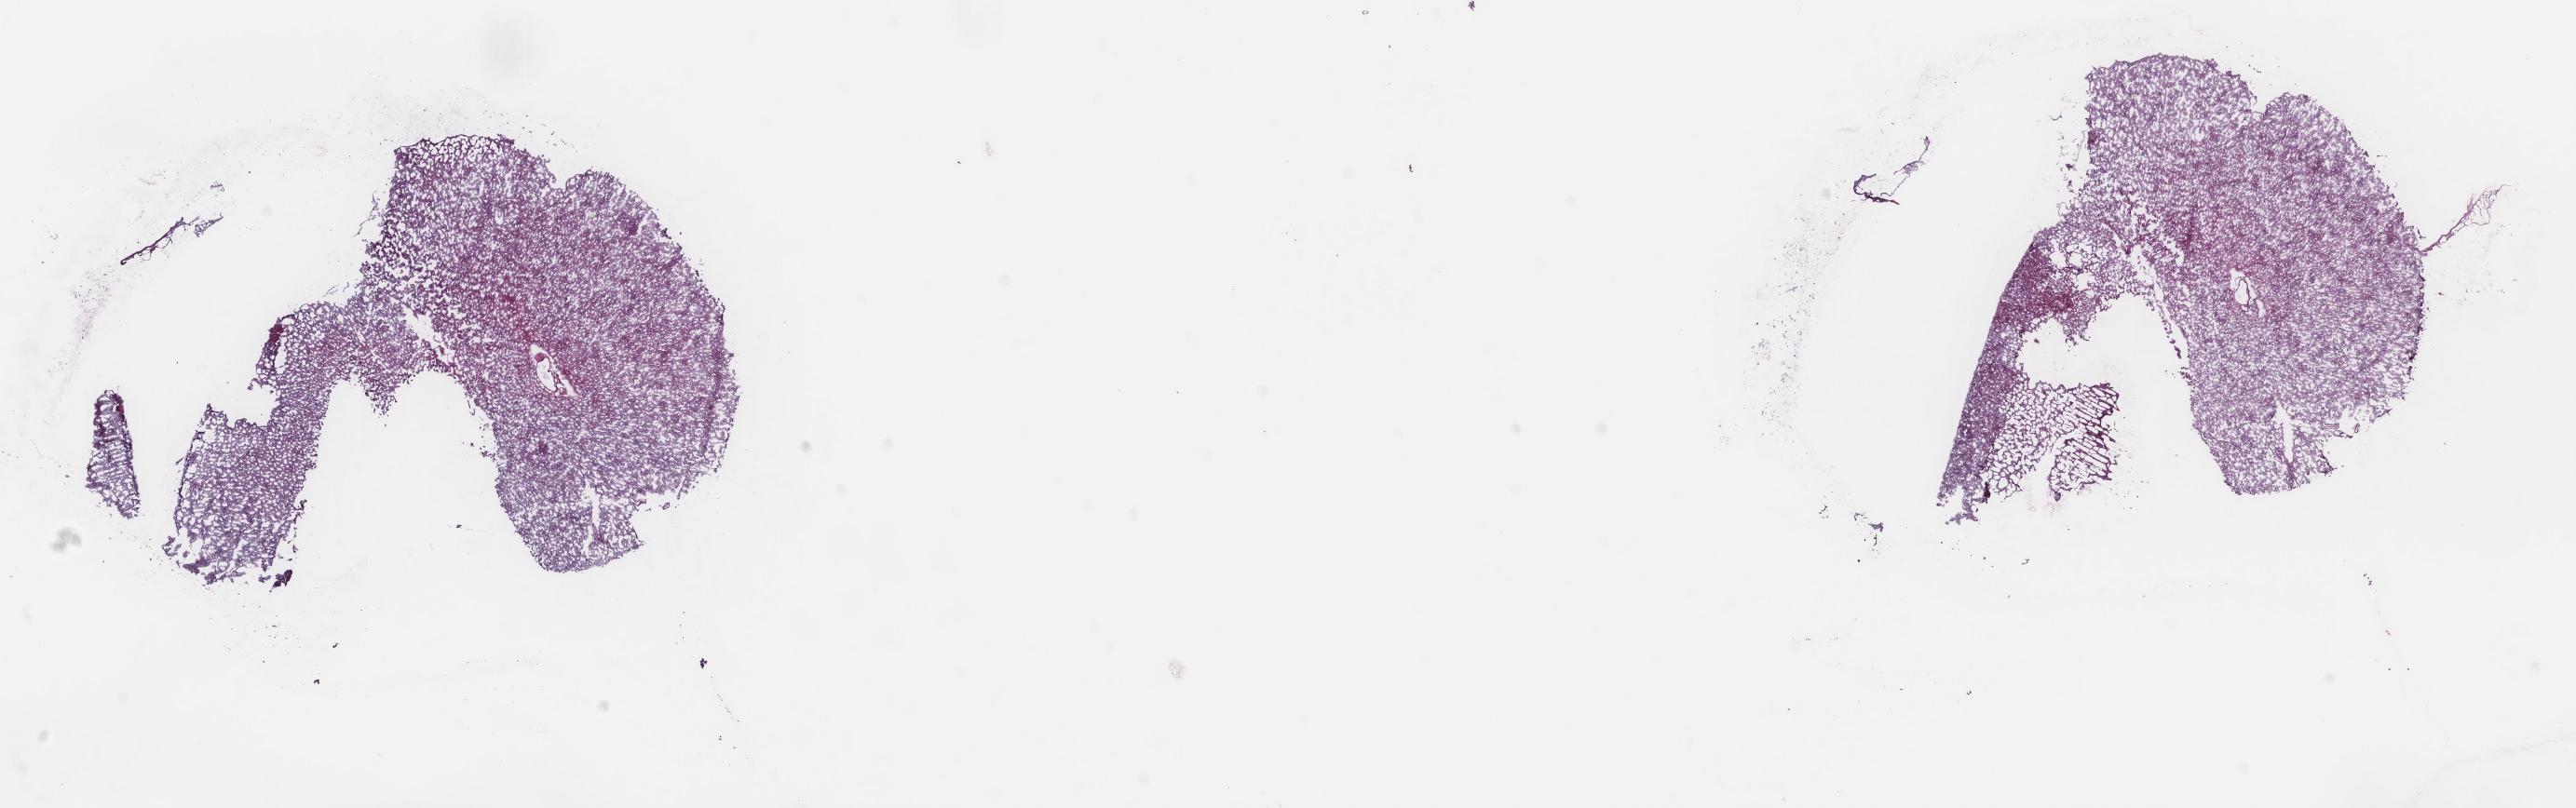
H&E-stained whole-slide image — low-resolution overview of the scanned area, about 22.0 x 6.9 mm. Frozen section from the top of the tissue portion. Brain, primary tumour sample. Female patient; age at initial diagnosis 34 years.
Diagnosis: Mixed glioma (cerebrum).